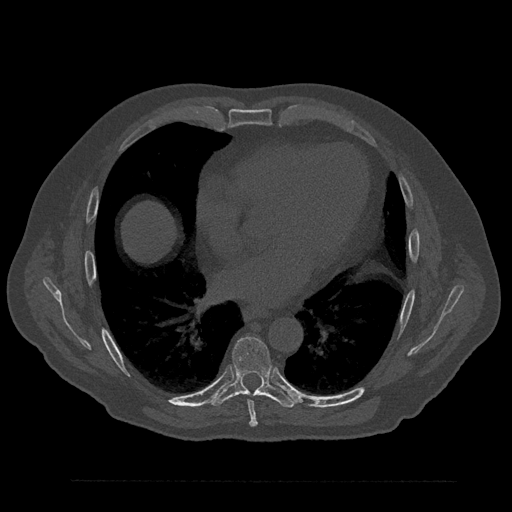
CT including the spine, one axial slice. Bone window (W 1800 / L 400 HU). 0.5 mm slice thickness. 512 × 512 image matrix, field of view 430 × 430 mm. Patient: male, 61 years. Case-level facts recorded for this patient, not image findings: primary cancer: prostate.
Structures marked on this image (semi-automatic segmentation, software-assisted and operator-edited):
- T7 vertebra: bounding box [x1, y1, x2, y2] px = [246, 394, 258, 427]
- T8 vertebra: [211, 336, 296, 408]